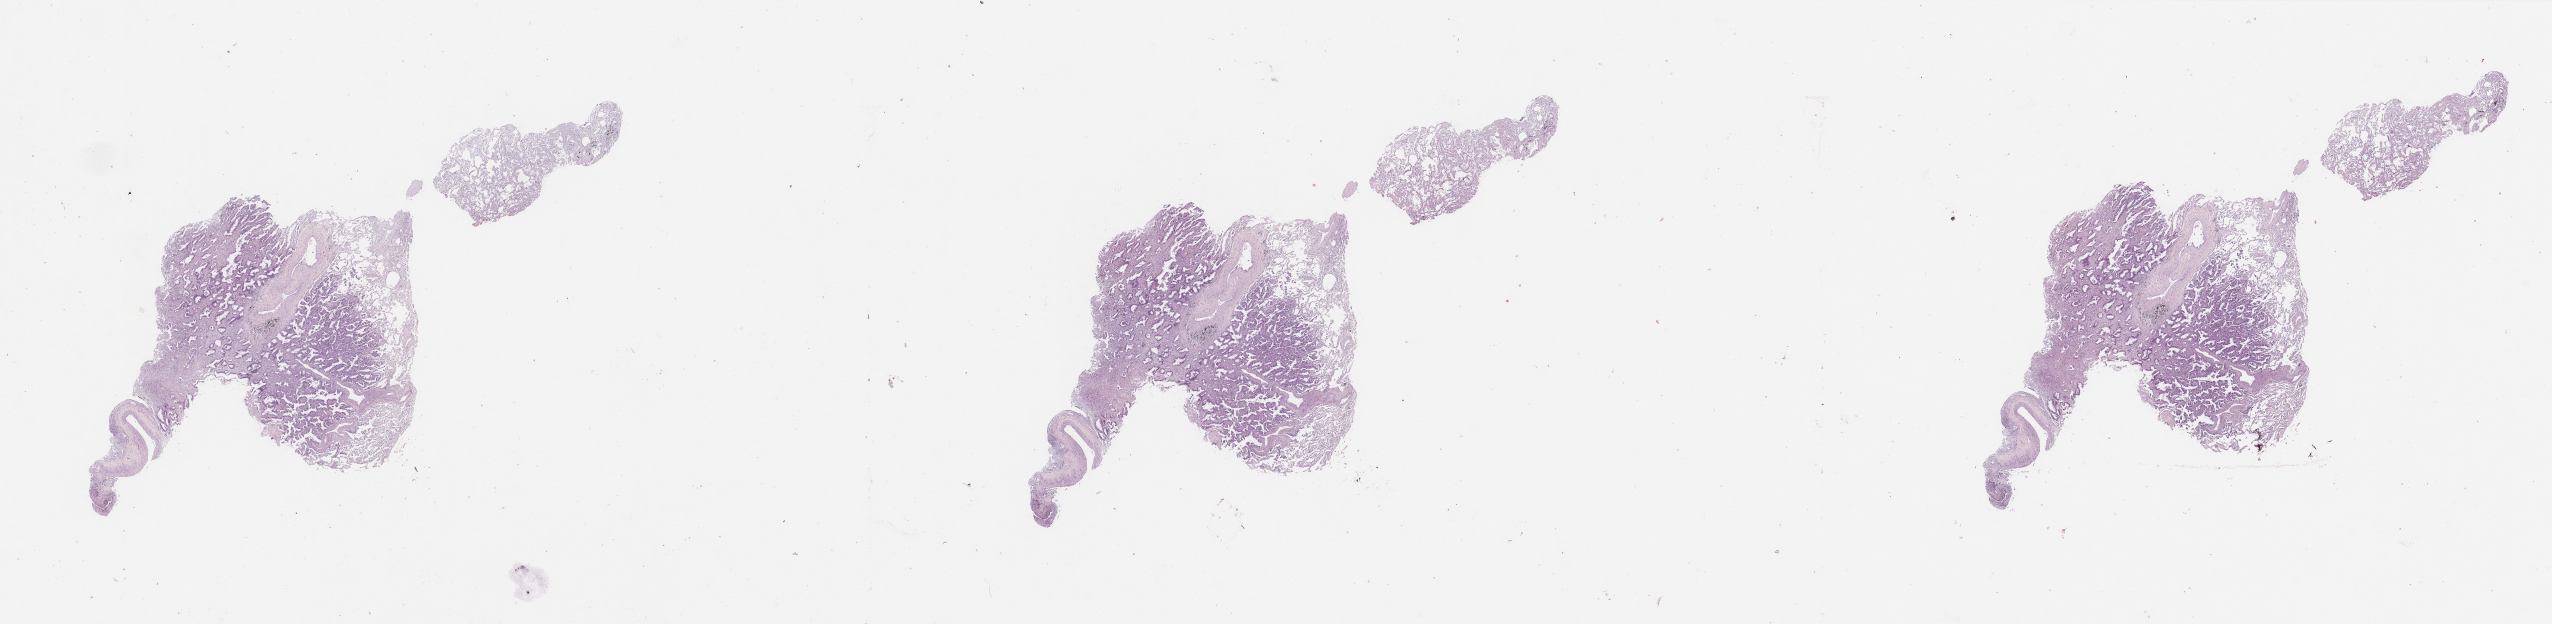
Digitized H&E tissue section (whole slide) — whole scanned area (about 40.4 x 9.9 mm) shown as a low-resolution overview. Tumour tissue sample, sampled site: lung. Patient: male, age 77 years. Histologic grade: G2 (moderately differentiated). Slide review estimates, as recorded: tumour nuclei 65%, necrosis 3%.
- diagnosis: Adenocarcinoma, NOS
- AJCC pathologic stage: IIIA